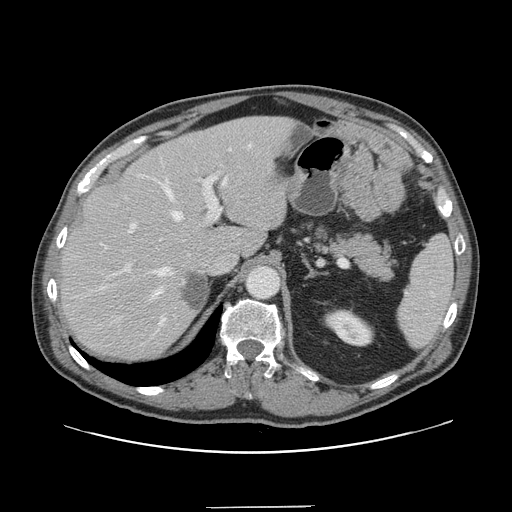
Contrast-enhanced abdominal CT, one axial slice. Position 103 of 139 along the scan axis. 120 kVp. Intravenous contrast given. Soft-tissue window (W 400 / L 40 HU). 2.5 mm slice thickness. 512 × 512 image matrix, field of view 397 × 397 mm. Male patient, age 64 years. Case-level facts recorded for this patient, not image findings: diagnosis: colorectal cancer liver metastases, imaged before liver resection; multiple liver metastases: yes; largest metastasis: 3.5 cm; chemotherapy before resection: yes.
Outlined on this slice (outlined manually by an expert reader):
- hepatic veins: box from (x=99, y=145) to (x=251, y=325) px
- liver: (x=62, y=118)–(x=293, y=358)
- planned liver remnant (the part of the liver to remain after resection): (x=61, y=118)–(x=275, y=358)
- portal vein (with intrahepatic branches): (x=113, y=148)–(x=231, y=275)
- liver metastasis: (x=182, y=273)–(x=208, y=310)